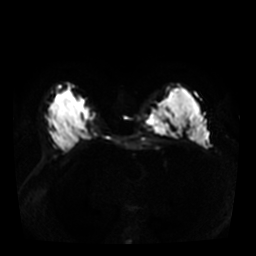
Breast MRI, one axial slice; slice 21 of 36 in the series (ordered by position); diffusion-weighted series; image 2 of 4 stored at this slice position (different b-values; order by instance number); 3 T; 5 mm slice thickness; 256 × 256 image matrix, field of view 340 × 340 mm. Female patient.
Structures marked on this image (expert manual segmentation):
- tumour on diffusion-weighted imaging: bounding box [x1, y1, x2, y2] px = [147, 99, 168, 134]